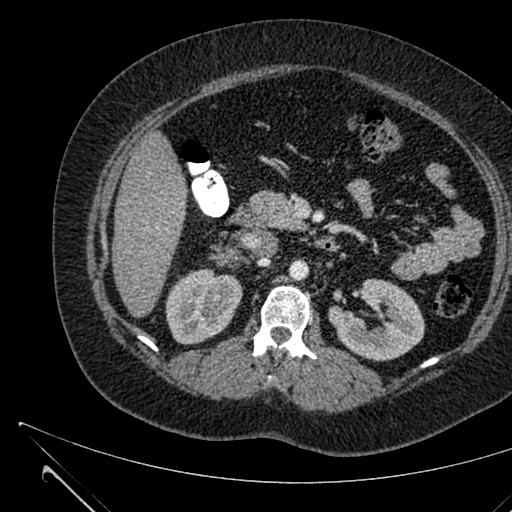
Contrast-enhanced abdominal CT, one axial slice; 120 kVp; intravenous contrast given; soft-tissue window (W 400 / L 40 HU); 512 × 512 image matrix. Patient: female, 36 years. Case-level facts recorded for this patient, not image findings: diagnosis: adrenocortical carcinoma; tumour side: right adrenal.
Annotated regions visible in this slice (semi-automatically segmented with operator editing):
- mass: box from (x=221, y=250) to (x=236, y=262) px